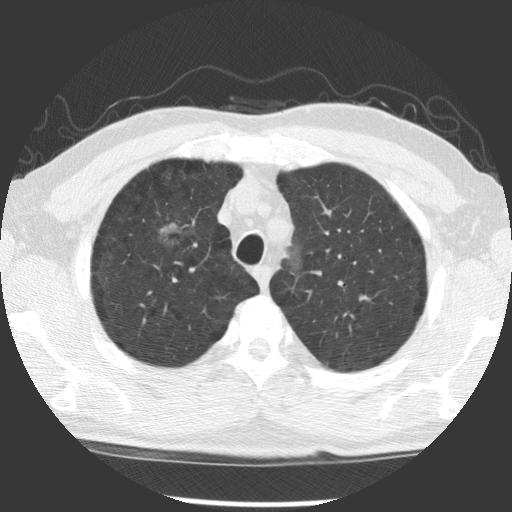
Axial slice from a low-dose chest CT screening exam; first (baseline) screen; lung window (W 1500 / L -600 HU); 2.5 mm slice thickness; standard (soft-tissue) reconstruction kernel (STANDARD); slice 92 of 122 in the series. Male, age 60 years at enrolment.
Lesion marked by an expert reader, box from (x=142, y=213) to (x=202, y=263) px. The exam's reader record, not a measurement of the box and not confirmed to be the same lesion: non-calcified nodule or mass ≥4 mm, right middle lobe, 20 × 20 mm, poorly defined margins, ground glass attenuation. Later outcome: lung cancer diagnosed 863 days after this screen — papillary adenocarcinoma, NOS, right upper lobe, moderately differentiated (G2), stage IB (AJCC 6th edition), 32 mm at pathology.